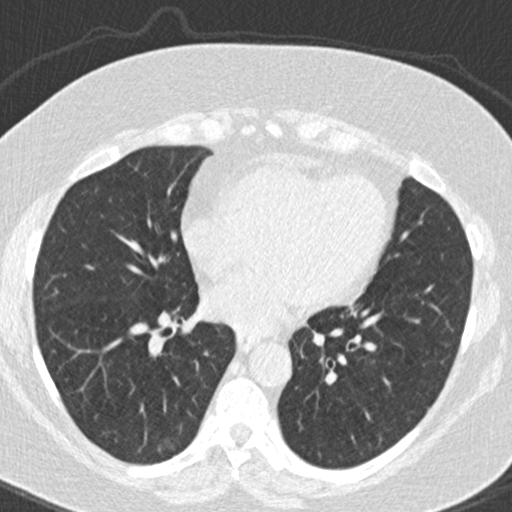
Axial slice from a low-dose chest CT screening exam. Baseline screening round. Lung window (W 1500 / L -600 HU). Standard (soft-tissue) reconstruction kernel (B30f). Female, age 63 years at enrolment. Former smoker at enrolment.
- Expert-annotated lung lesion, bounding box <145,428,191,464> (left, top, right, bottom; pixels).
- The exam's reader record, not a measurement of the box and not confirmed to be the same lesion: non-calcified nodule or mass ≥4 mm, right lower lobe, 16 × 10 mm, poorly defined margins, ground glass attenuation.
- Official screen result: positive, change unspecified: nodule(s) >= 4 mm or enlarging nodule(s), mass(es), or other non-specific abnormalities suspicious for lung cancer.
- Later outcome: lung cancer diagnosed 246 days after this screen — bronchiolo-alveolar adenocarcinoma, NOS, right lower lobe, well differentiated (G1), stage IA (AJCC 6th edition), 12 mm at pathology.